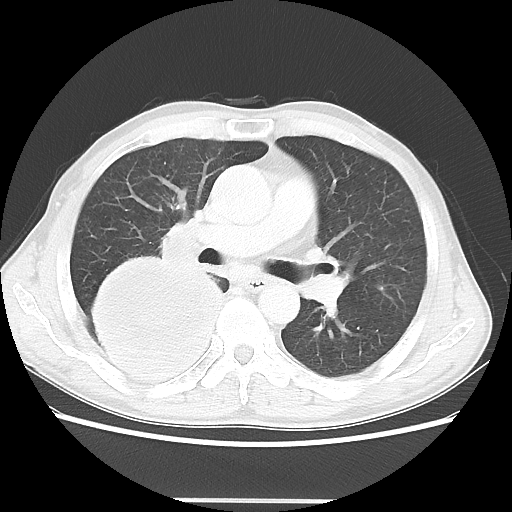
Chest CT, one axial slice; position 28 of 48 along the scan axis; reconstruction kernel LUNG; lung window (W 1500 / L -600 HU); 5 mm slice thickness; 512 × 512 image matrix, field of view 361 × 361 mm. Male patient, age 66 years. From the clinical record (not read from this slice): clinical TNM (as recorded): T4 N1 M1.
Annotated regions visible in this slice (bounding box drawn by a radiologist):
- lung tumour (recorded histology: small cell carcinoma): box from (x=79, y=254) to (x=228, y=389) px